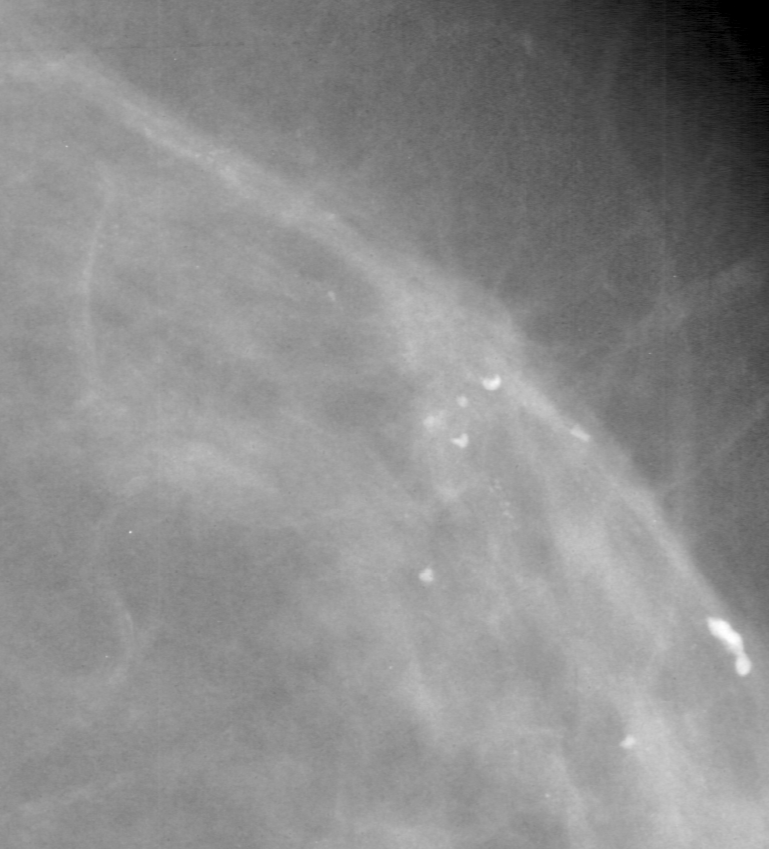
Region of interest cut from a scanned film mammogram (one marked finding), right breast, CC view.
Marked abnormality: calcifications, morphology pleomorphic, distribution linear; BI-RADS assessment category 4; subtlety rating 2 on a 1 (subtle) to 5 (obvious) scale; pathology result (as recorded, not read from the image): malignant.